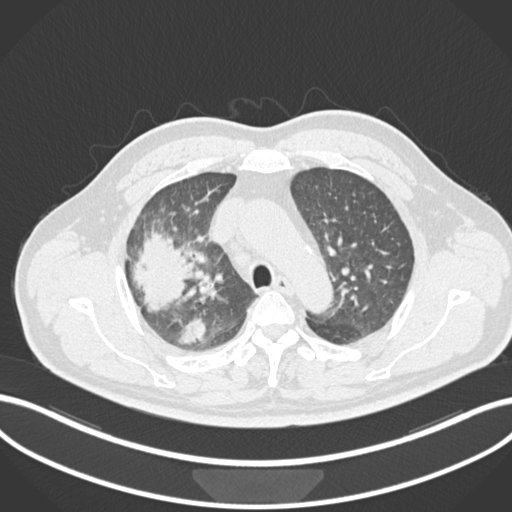
Chest CT, one axial slice; slice 670 of 852 in the series (ordered by position); reconstruction kernel B30f; lung window (W 1500 / L -600 HU); 1 mm slice thickness; 512 × 512 image matrix. Patient: male, 55 years. Case-level facts recorded for this patient, not image findings: clinical TNM (as recorded): T3 N2 M1.
Structures marked on this image (bounding box drawn by a radiologist):
- lung tumour (recorded histology: adenocarcinoma): bounding box <132,225,192,316> (left, top, right, bottom; pixels)